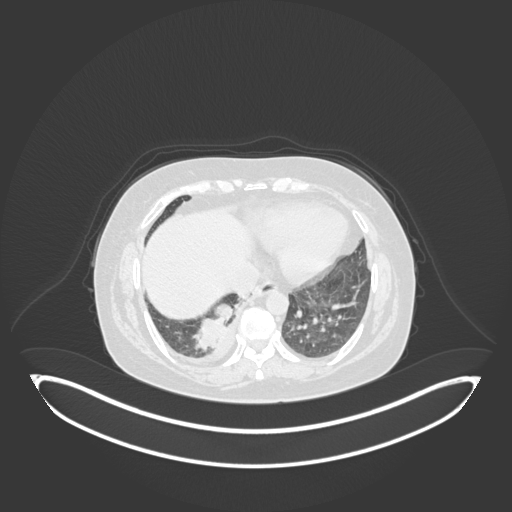
Chest CT, one axial slice; slice 37 of 231 in the series (ordered by position); reconstruction kernel B30f; lung window (W 1500 / L -600 HU); 1 mm slice thickness; 512 × 512 image matrix, field of view 500 × 500 mm. Female patient, age 56 years. From the clinical record (not read from this slice): clinical TNM (as recorded): T2b N1 M0; histopathological grade: G3.
Structures marked on this image (bounding box drawn by a radiologist):
- lung tumour (recorded histology: small cell carcinoma): bounding box [x1, y1, x2, y2] px = [190, 293, 244, 359]